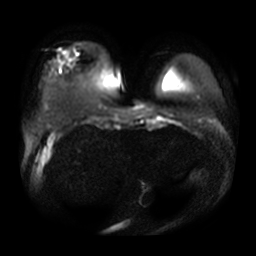
Breast MRI, one axial slice; position 7 of 29 along the scan axis; diffusion-weighted series; image 2 of 4 stored at this slice position (different b-values; order by instance number); 3 T; 5 mm slice thickness; 256 × 256 image matrix, field of view 380 × 380 mm. Female patient.
Structures marked on this image (outlined manually by an expert reader):
- tumour on diffusion-weighted imaging: bounding box [x1, y1, x2, y2] px = [65, 58, 70, 63]